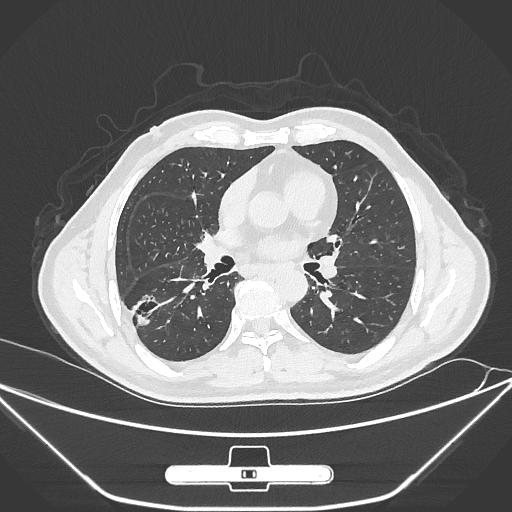
Chest CT, one axial slice. Reconstruction kernel IMR1,SharpPlus. Lung window (W 1500 / L -600 HU). 1 mm slice thickness. 512 × 512 image matrix, field of view 398 × 398 mm. Male patient, age 71 years. Case-level facts recorded for this patient, not image findings: clinical TNM (as recorded): T1c N0 M0; histopathological grade: G2.
Structures marked on this image (rectangle marked by the reading radiologist):
- lung tumour (recorded histology: adenocarcinoma): bounding box <125,288,165,338> (left, top, right, bottom; pixels)